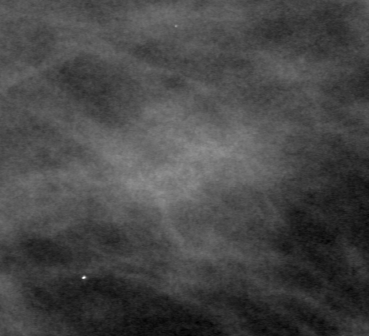
Cropped region of a digitized screen-film mammogram centred on a radiologist-marked abnormality, right breast, MLO view.
Finding: mass, shape oval, margins ill defined; BI-RADS assessment category 4; subtlety rating 3 on a 1 (subtle) to 5 (obvious) scale; pathology result (as recorded, not read from the image): benign.